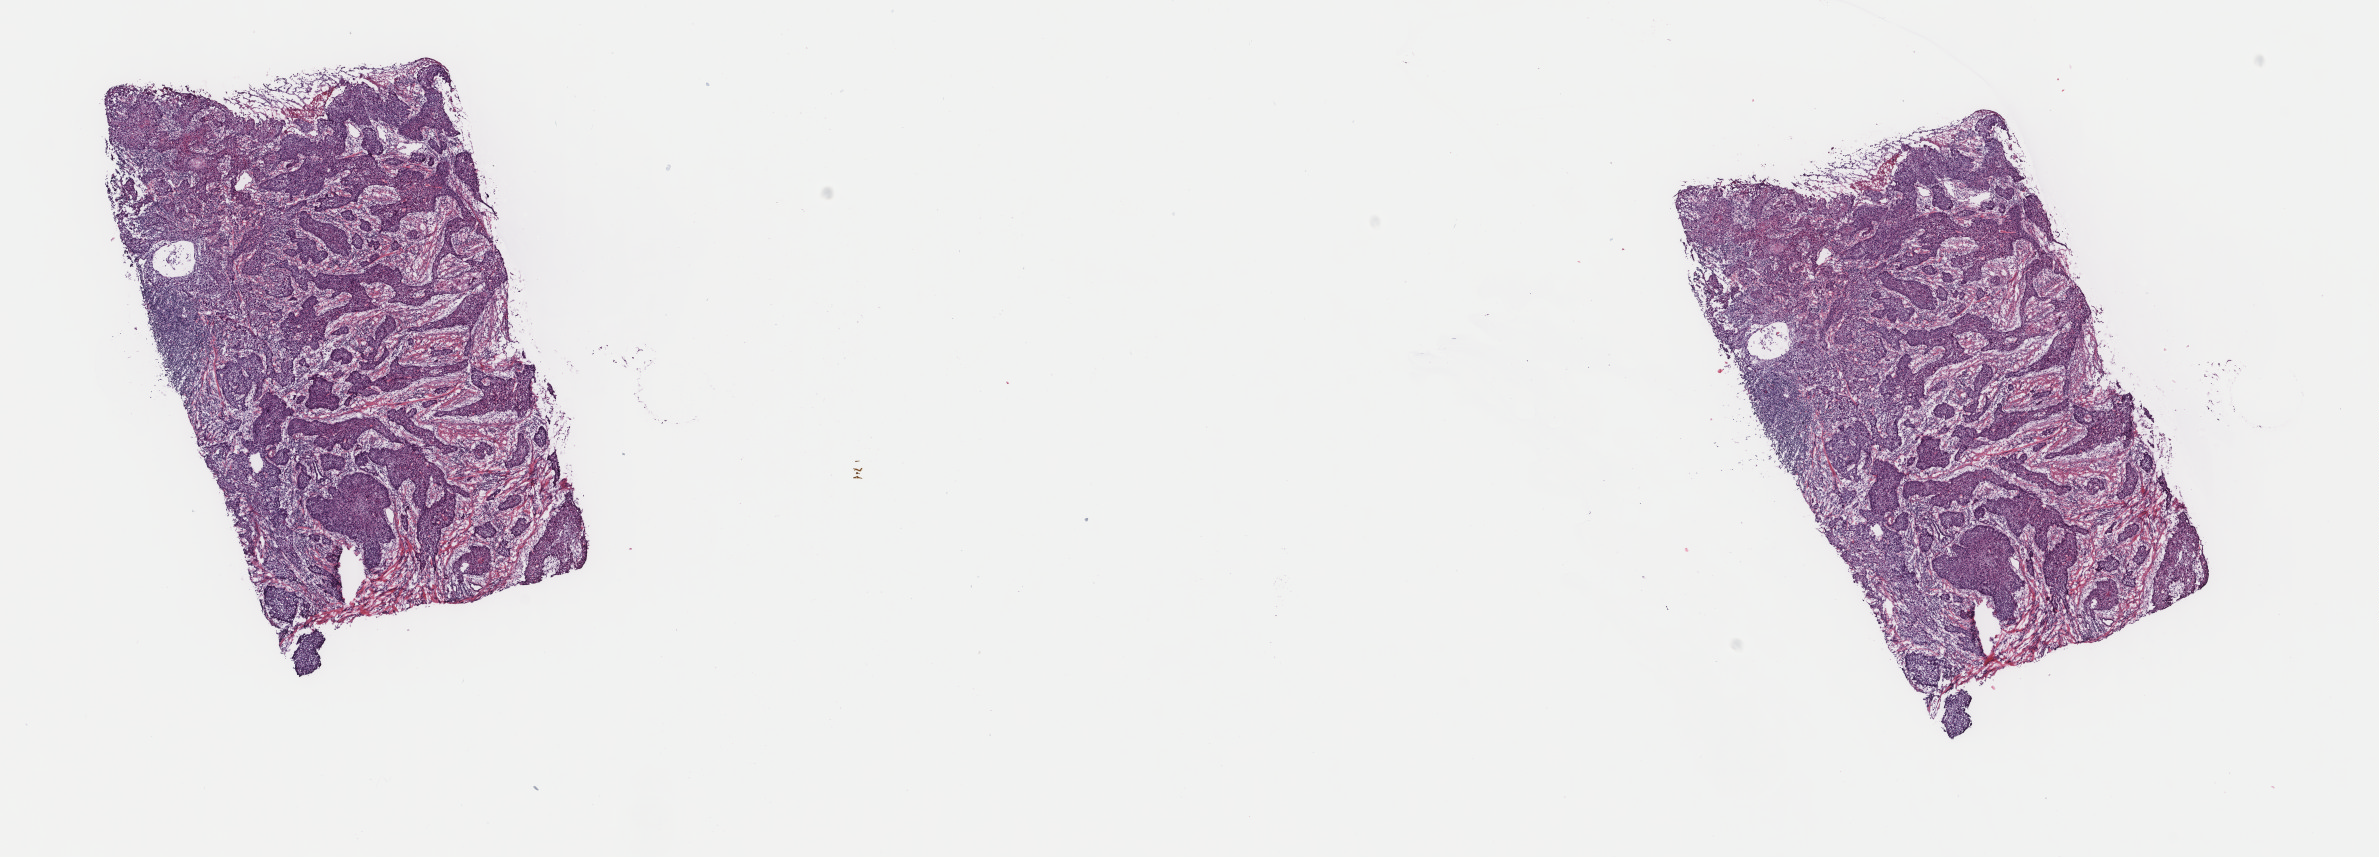
Whole-slide histology image, H&E — whole scanned area (about 18.9 x 6.8 mm) shown as a low-resolution overview; frozen section from the top of the tissue portion; sample: primary tumour, head and neck. Male, age 67 years at initial diagnosis. Histologic grade: G3 (poorly differentiated). Pathologist review of this section (percent, as recorded): tumour cells 75%, tumour nuclei 75%, normal cells 0%, stromal cells 25%, necrosis 0%. Inflammatory infiltration, as recorded: lymphocyte infiltration 20%, monocyte infiltration 0%, neutrophil infiltration 0%.
- AJCC pathologic stage: IVA (7th edition)
- laterality: midline
- diagnosis: Squamous cell carcinoma, keratinizing, NOS
- TNM: T4a N0 M0